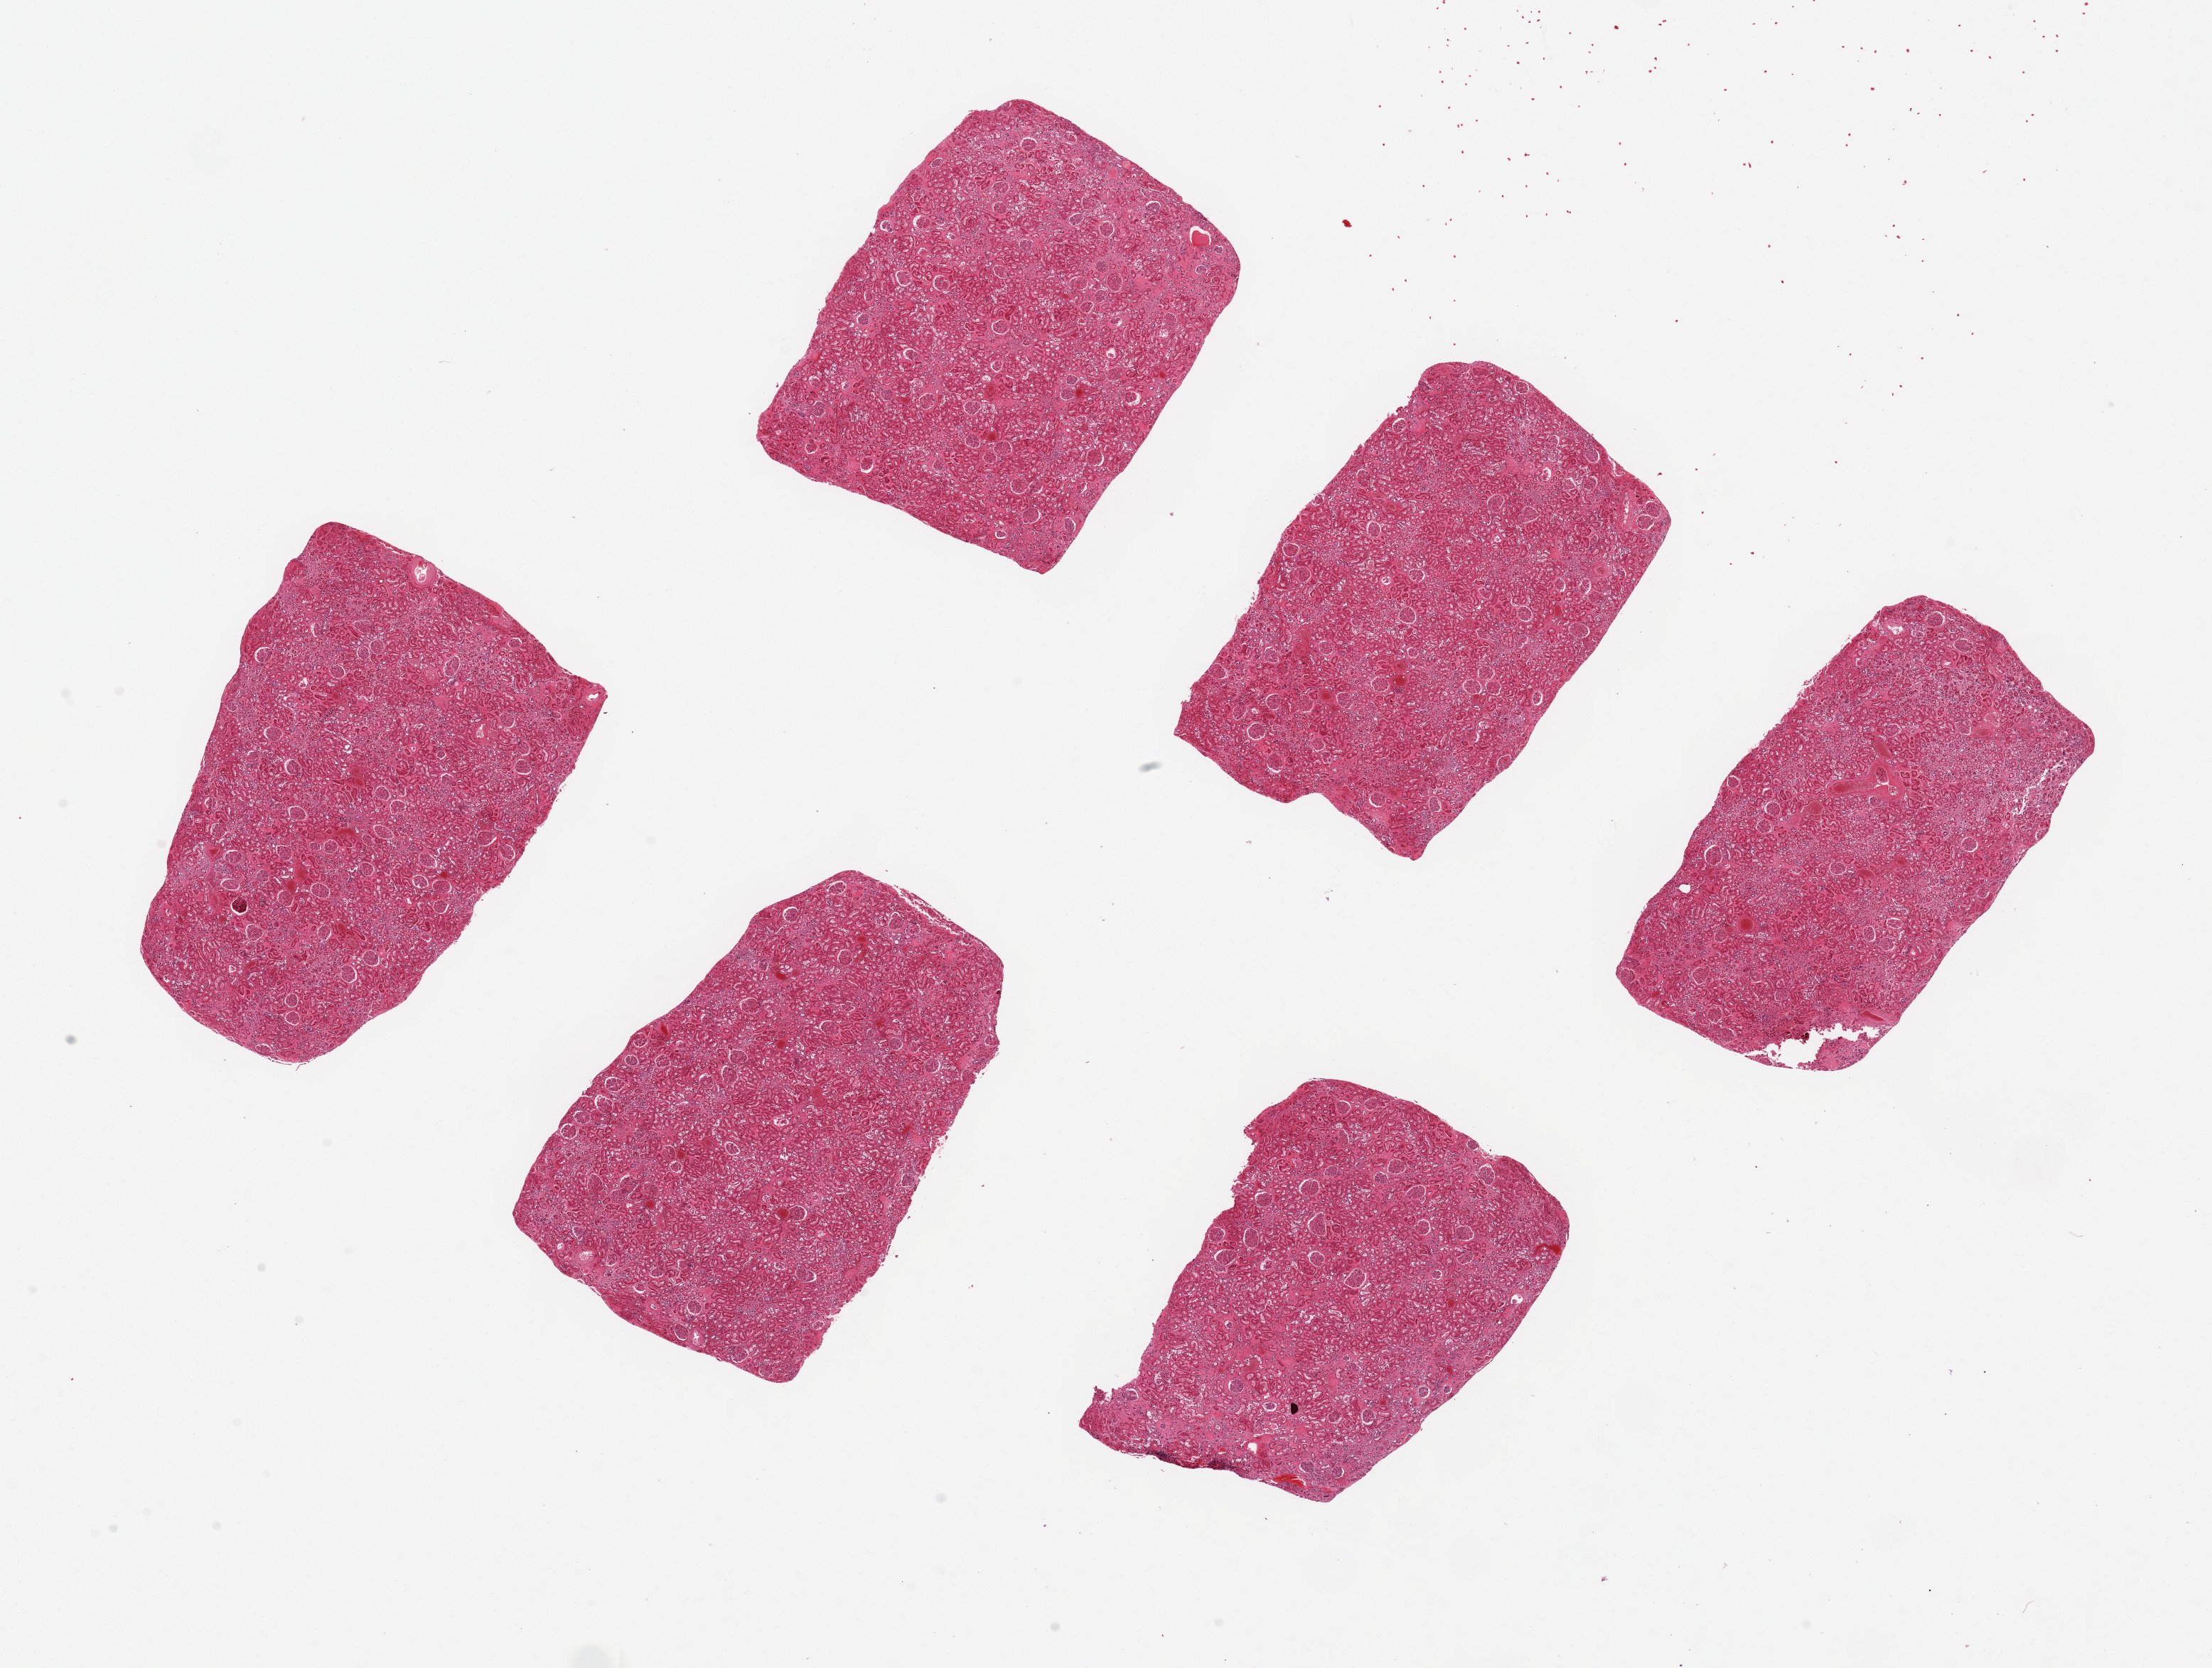
Digitized haematoxylin and eosin-stained section, brightfield — a low-resolution overview of the entire scanned area, about 24.6 x 18.6 mm (from a 20x scan), PAXgene-fixed, paraffin-embedded tissue, target tissue: renal cortex, tissue donor sample. Female donor.
Pathologist's review note for this sample: 6 pieces up to 5.6x3.7 mm; all contain cortex; no lesions.